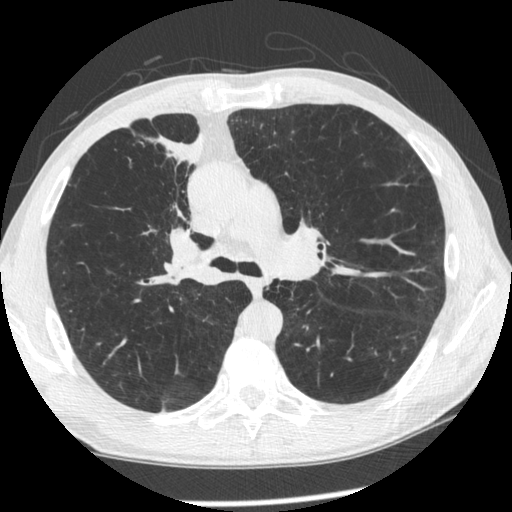
Low-dose screening chest CT, one axial slice; slice 147 of 261 in the series (ordered by position); reconstruction kernel STANDARD; lung window (W 1500 / L -600 HU); 512 × 512 image matrix, field of view 340 × 340 mm.
Annotated regions visible in this slice (outlined manually by an expert reader):
- lesion 1 (tumor, upper lobe of right lung): box from (x=151, y=134) to (x=206, y=236) px